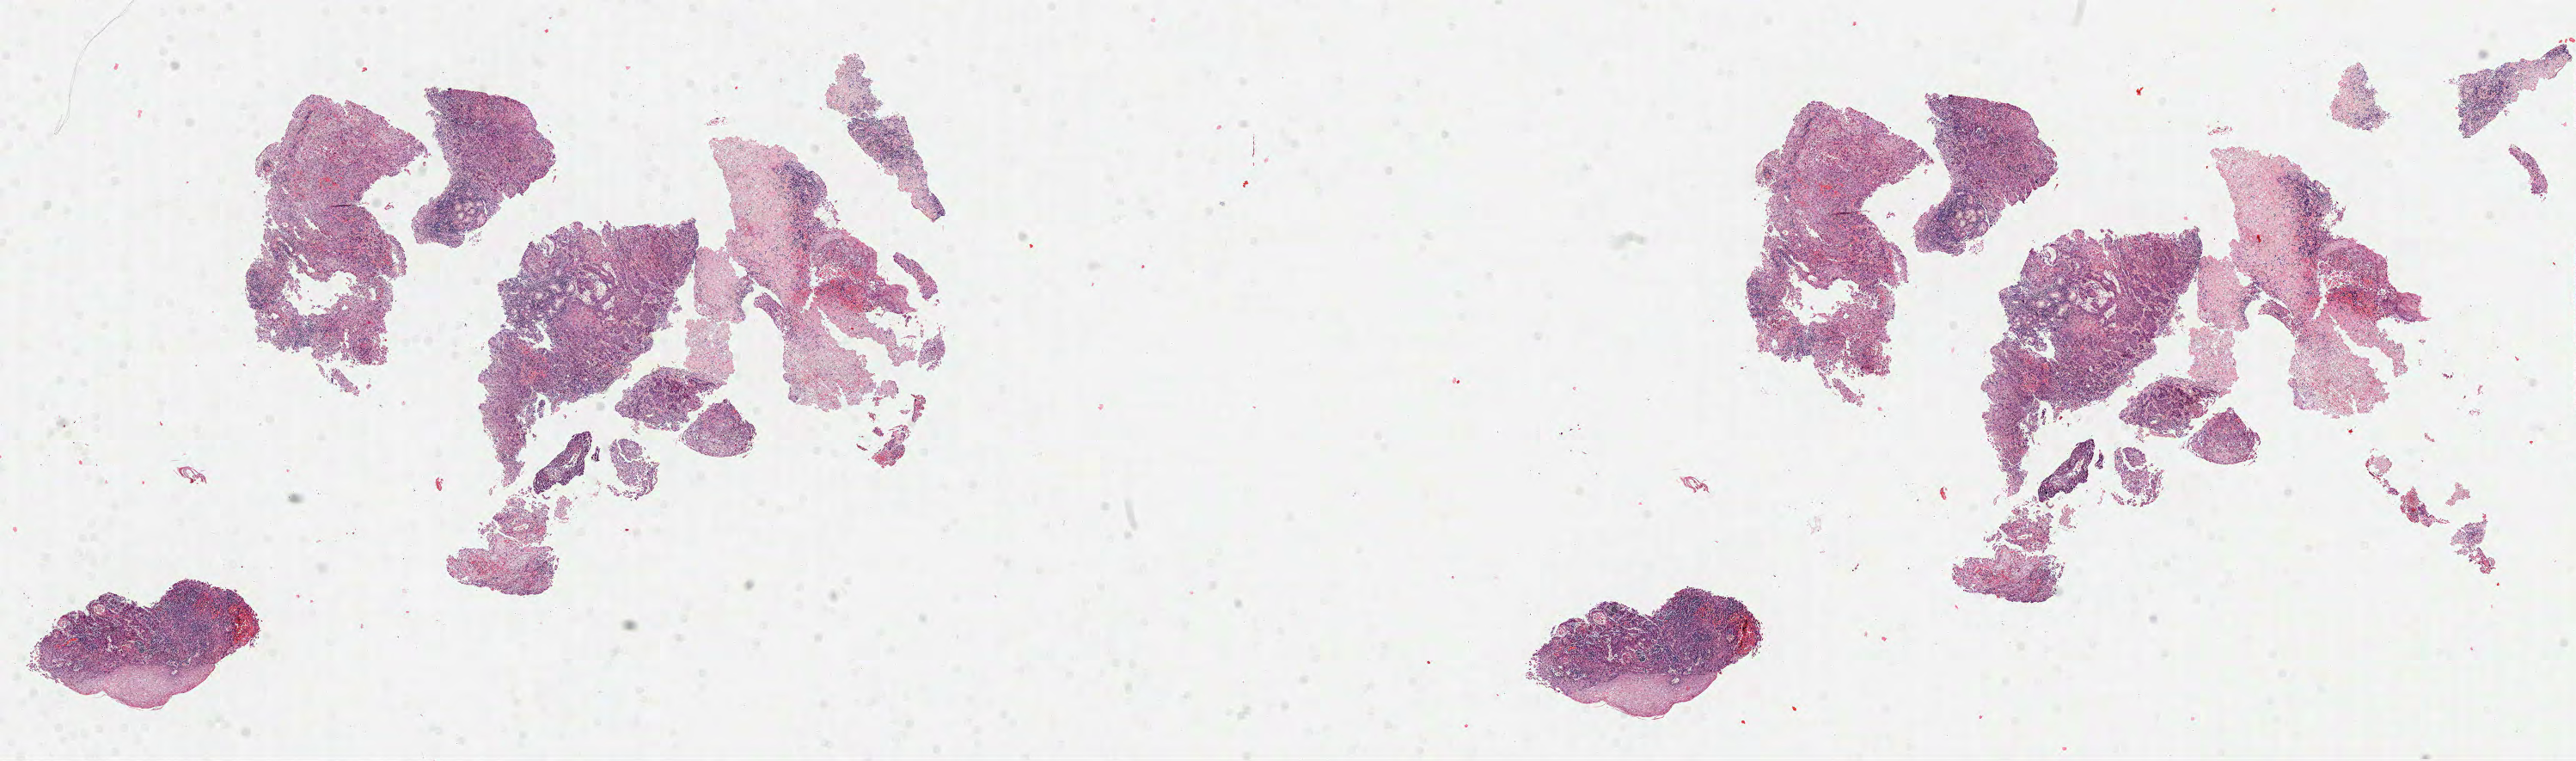
Whole-slide histology image, H&E-stained, a low-resolution overview of the entire scanned area, about 24.2 x 7.1 mm, formalin-fixed paraffin-embedded (FFPE) diagnostic section, sample: primary tumour, head and neck. Female, age 60 years at initial diagnosis. Histologic grade: G2 (moderately differentiated).
Histologic diagnosis: Squamous cell carcinoma, NOS (larynx, NOS).